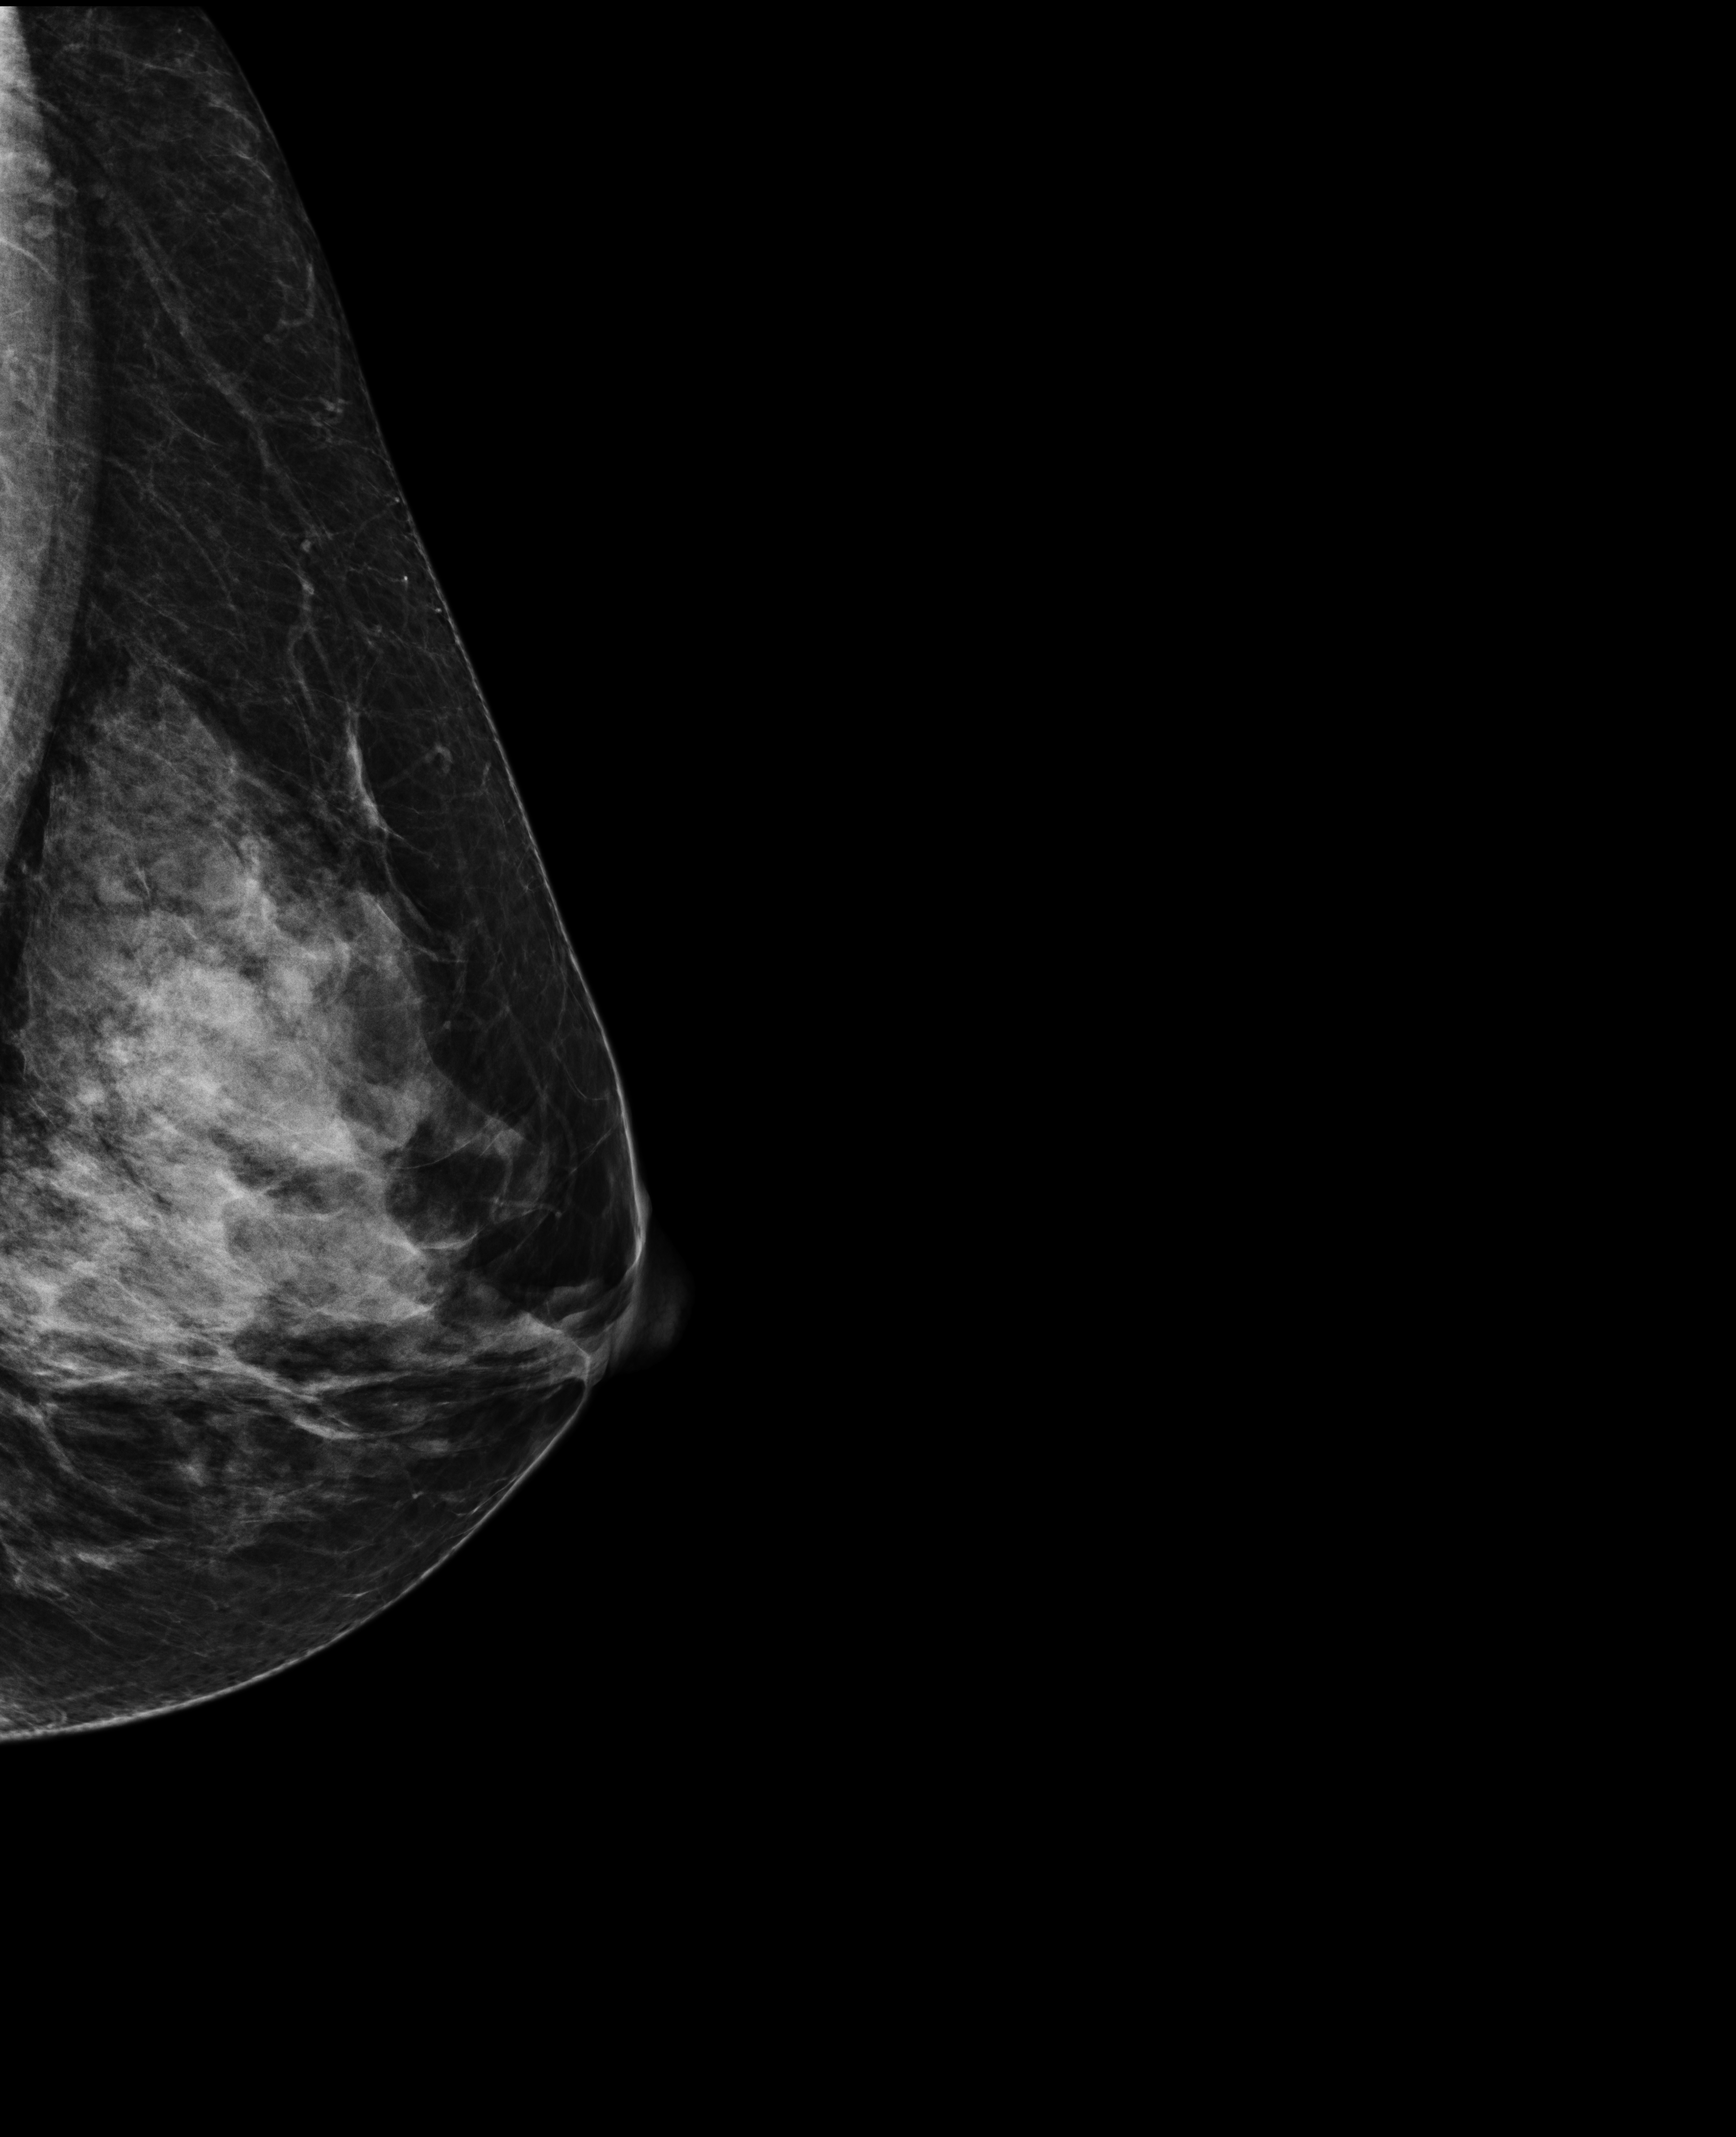
Digital mammogram (FFDM); left breast; laterally exaggerated craniocaudal (XCCL) view; screening examination; system: Selenia Dimensions. Patient aged 50 years (female).
Breast density at the screening exam (both breasts): extremely dense (BI-RADS density category d). Final BI-RADS assessment for this screening round (tomosynthesis exam, both breasts): category 1. Recall: no recall after this screen.